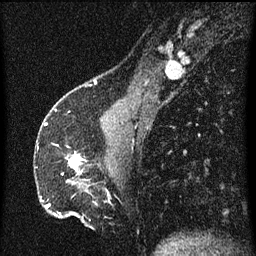
Breast MRI (dynamic contrast-enhanced), one sagittal slice; slice 20 of 60 in the series (ordered by position); dynamic contrast-enhanced series, image 2 of 3 at this slice position (ordered by acquisition); 1.5 T; TE 4.2 ms, TR 8 ms; 2 mm slice thickness; 256 × 256 image matrix, field of view 180 × 180 mm. Patient: female, 51 years.
Annotated regions visible in this slice (semi-automatically segmented with operator editing):
- analysis volume of interest (the breast-tissue region the enhancement analysis was run in; not a lesion): bounding box [x1, y1, x2, y2] px = [66, 154, 85, 175]
- tumour enhancement mask (voxels above the 70 % enhancement threshold inside the analysis volume of interest): [70, 156, 85, 171]